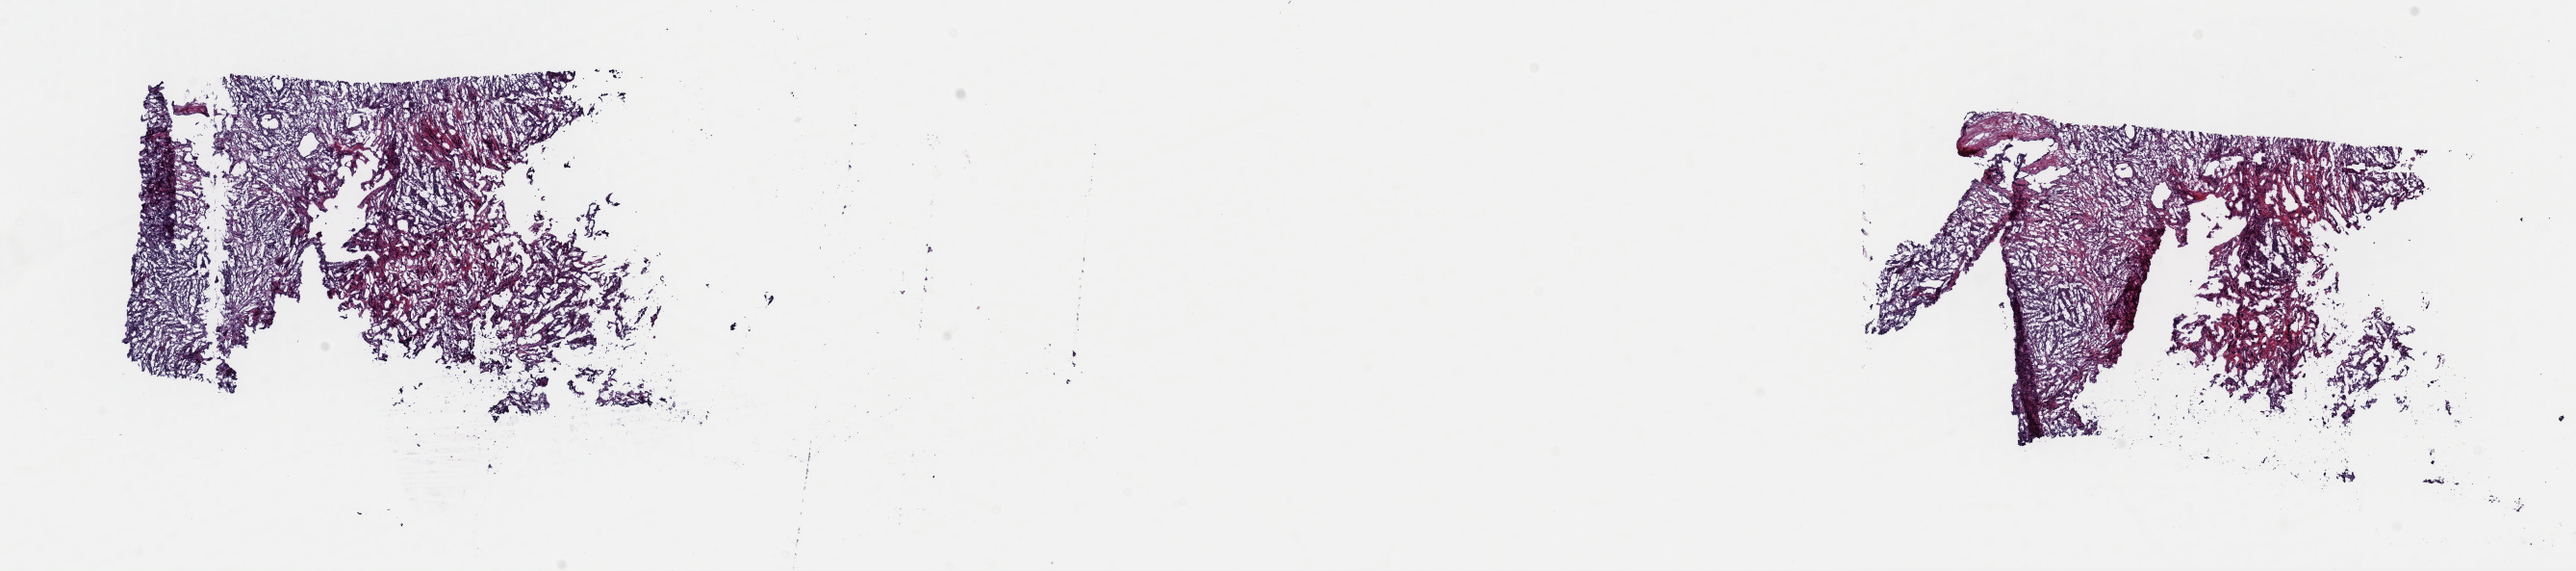
Whole-slide histology image, H&E, a low-resolution overview of the entire scanned area, about 21.1 x 4.7 mm, frozen section from the top of the tissue portion, primary tumour sample from the prostate. Male, age 64 years at initial diagnosis. Gleason score: 9 (4+5). Pathologist review of this section (percent, as recorded): tumour cells 100%, tumour nuclei 75%, normal cells 0%, stromal cells 0%, necrosis 0%. Inflammatory infiltration, as recorded: lymphocyte infiltration 2%, monocyte infiltration 0%, neutrophil infiltration 0%.
Laterality: bilateral. Histologic diagnosis: Adenocarcinoma, NOS.